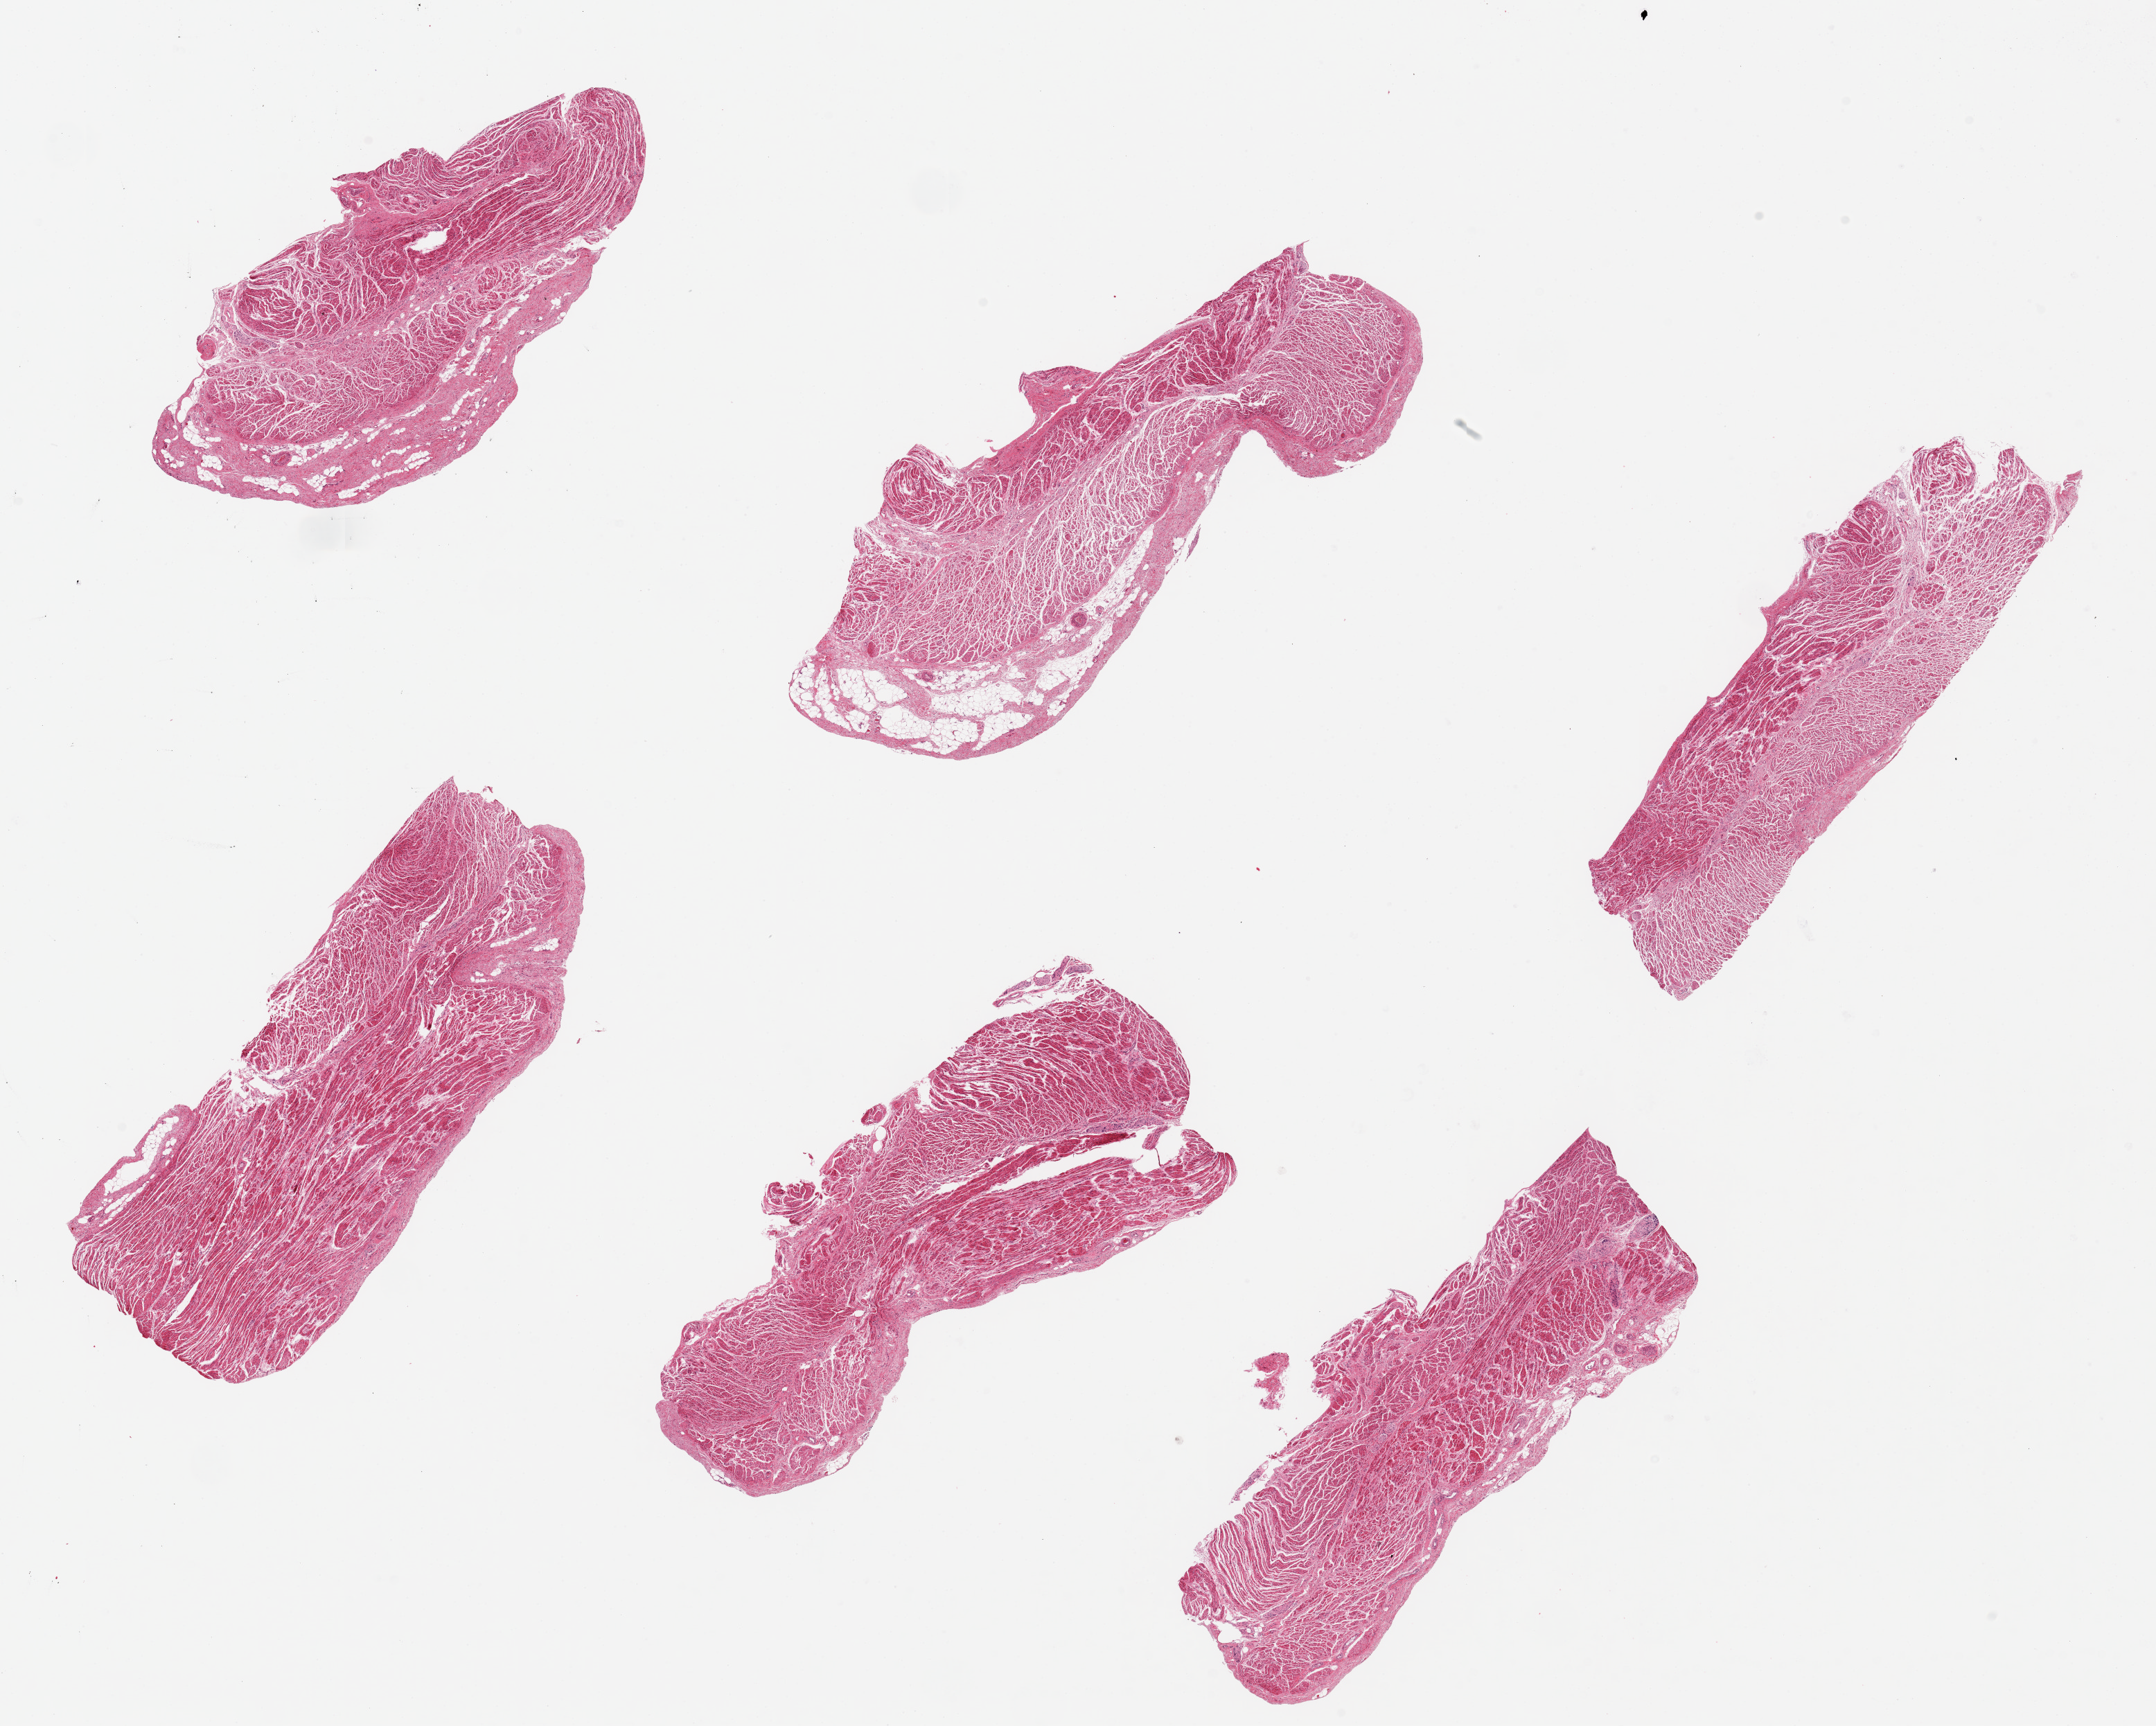
Digitized haematoxylin and eosin-stained section, low-resolution overview of the scanned area, about 24.6 x 19.7 mm (from a 20x scan); PAXgene-fixed, paraffin-embedded tissue; target tissue: gastroesophageal junction; donor tissue sample.
Reviewer comment on this tissue sample: 6 pieces, up to 8x3mm; all muscle with 1 mm adipose in 1 piece.